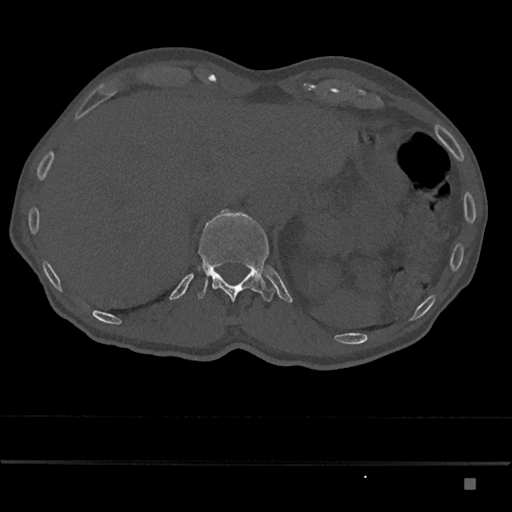
CT including the spine, one axial slice; position 614 of 797 along the scan axis; reconstruction kernel Br40s/3; bone window (W 1800 / L 400 HU); 0.5 mm slice thickness; 512 × 512 image matrix, field of view 390 × 390 mm. Patient: male, 72 years. From the clinical record (not read from this slice): primary cancer: prostate.
Outlined on this slice (semi-automatic segmentation, software-assisted and operator-edited):
- T12 vertebra: bounding box (x1, y1, x2, y2) in pixels: (197, 211, 276, 302)